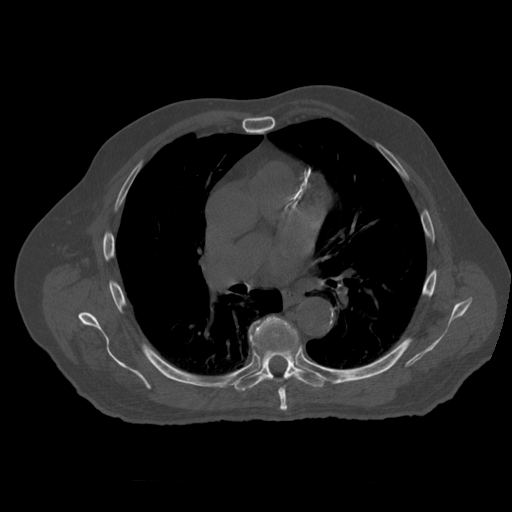
CT including the spine, one axial slice. Position 370 of 399 along the scan axis. Reconstruction kernel STANDARD. 120 kVp. Bone window (W 1800 / L 400 HU). 1.25 mm slice thickness. 512 × 512 image matrix. Patient age 73 years. Case-level facts recorded for this patient, not image findings: primary cancer: prostate; vertebrae with lytic lesions (as recorded): L2.
Outlined on this slice (semi-automatic segmentation, software-assisted and operator-edited):
- T6 vertebra: bounding box (x1, y1, x2, y2) in pixels: (254, 317, 289, 412)
- T7 vertebra: (234, 317, 330, 391)